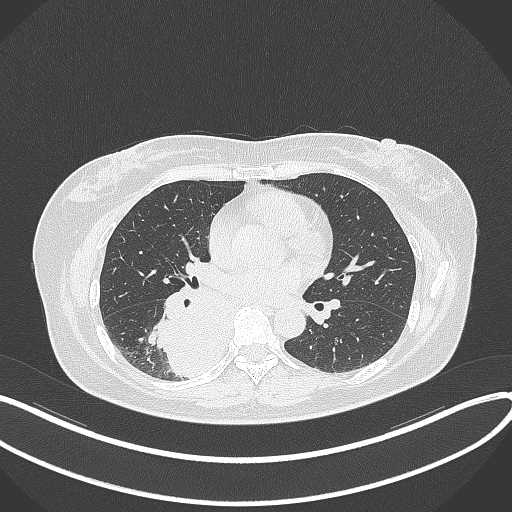
Chest CT, one axial slice; position 177 of 331 along the scan axis; reconstruction kernel B70f; 120 kVp; lung window (W 1500 / L -600 HU); 1 mm slice thickness; 512 × 512 image matrix, field of view 400 × 400 mm. Female patient, age 54 years. Case-level facts recorded for this patient, not image findings: clinical TNM (as recorded): T4 N0 M0.
Annotated regions visible in this slice (bounding box drawn by a radiologist):
- lung tumour (recorded histology: adenocarcinoma): bounding box <151,285,240,382> (left, top, right, bottom; pixels)